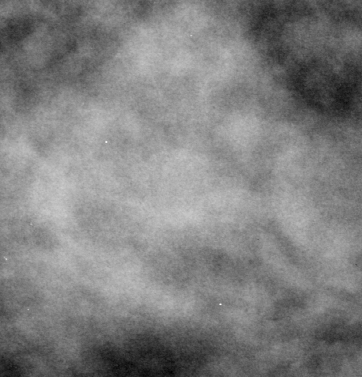
Region of interest cut from a scanned film mammogram (one marked finding); left breast; MLO view.
Finding: mass, shape oval, margins circumscribed / obscured; BI-RADS assessment category 4; subtlety rating 2 on a 1 (subtle) to 5 (obvious) scale; pathology (as recorded): benign.